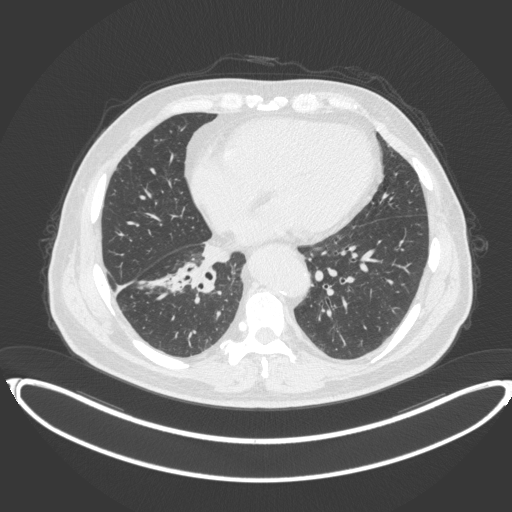
Chest CT, one axial slice. Slice 156 of 383 in the series (ordered by position). Lung window (W 1500 / L -600 HU). 512 × 512 image matrix. Patient: male, 61 years. From the clinical record (not read from this slice): clinical TNM (as recorded): T1b N1 M0.
Annotated regions visible in this slice (bounding box drawn by a radiologist):
- lung tumour (recorded histology: squamous cell carcinoma): box from (x=167, y=258) to (x=216, y=297) px